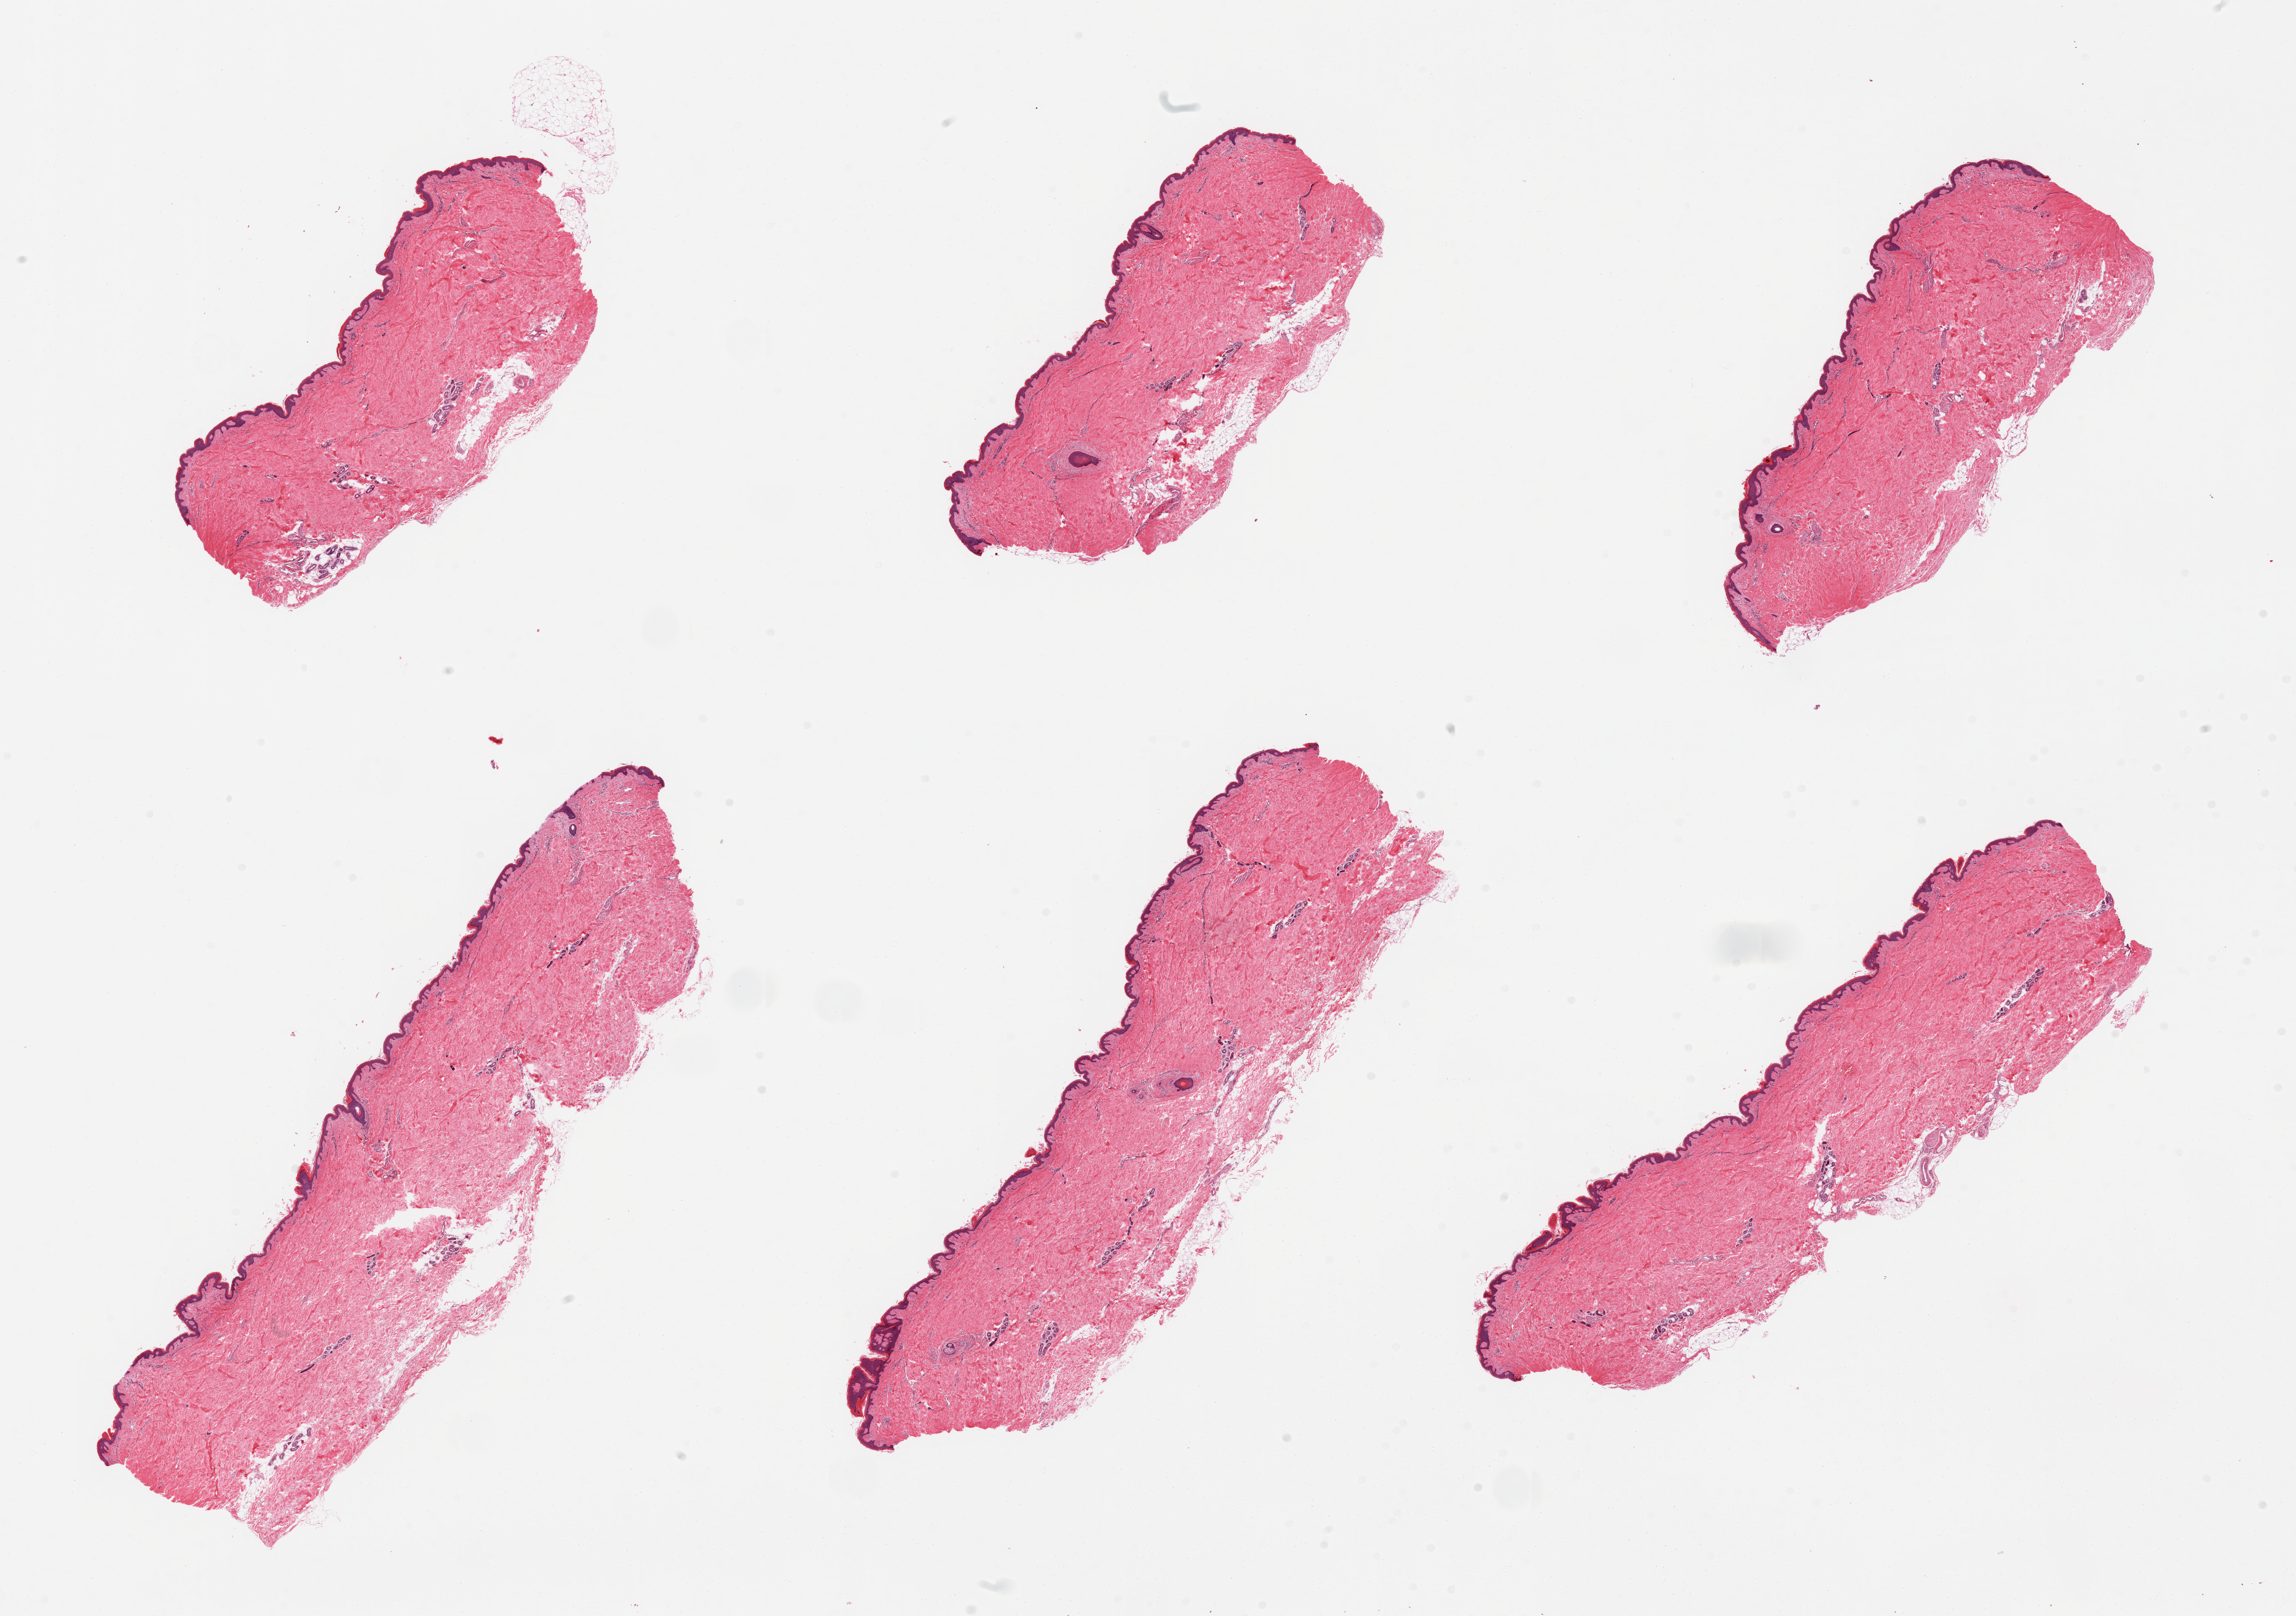
Hematoxylin and eosin (H&E) whole-slide image — a low-resolution overview of the entire scanned area, about 29.5 x 20.8 mm (acquisition: 20x scan); PAXgene-fixed, paraffin-embedded tissue; sampled site (target tissue): skin of suprapubic region; tissue donor sample. Donor: male.
Review note (as recorded): 6 pieces; well trimmed.